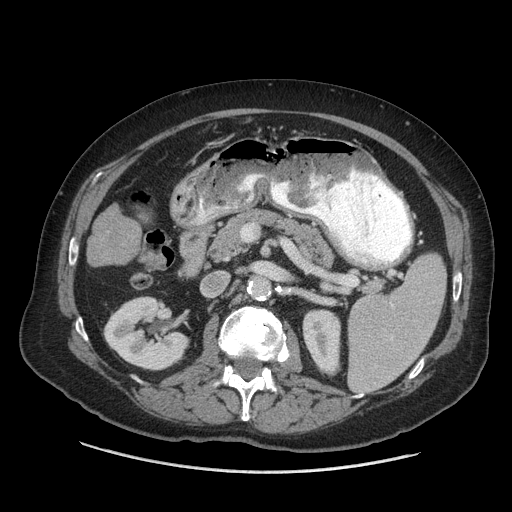
Contrast-enhanced abdominal CT (liver protocol), one axial slice. Position 21 of 77 along the scan axis. Reconstruction kernel STANDARD. Soft-tissue window (W 400 / L 40 HU). 2.5 mm slice thickness. 512 × 512 image matrix. Case-level facts recorded for this patient, not image findings: diagnosis: hepatocellular carcinoma (patient treated with transarterial chemoembolisation; whether this scan precedes or follows treatment is not stated here); TNM stage (as recorded): Stage-I; Child-Pugh class: A; tumour differentiation: well differentiated; tumour nodularity: uninodular.
Structures marked on this image (semi-automatically segmented with operator editing):
- liver parenchyma outside the tumour (the mass and vessels are separate outlines, so this box may not span the whole liver): bounding box [x1, y1, x2, y2] px = [95, 206, 124, 230]